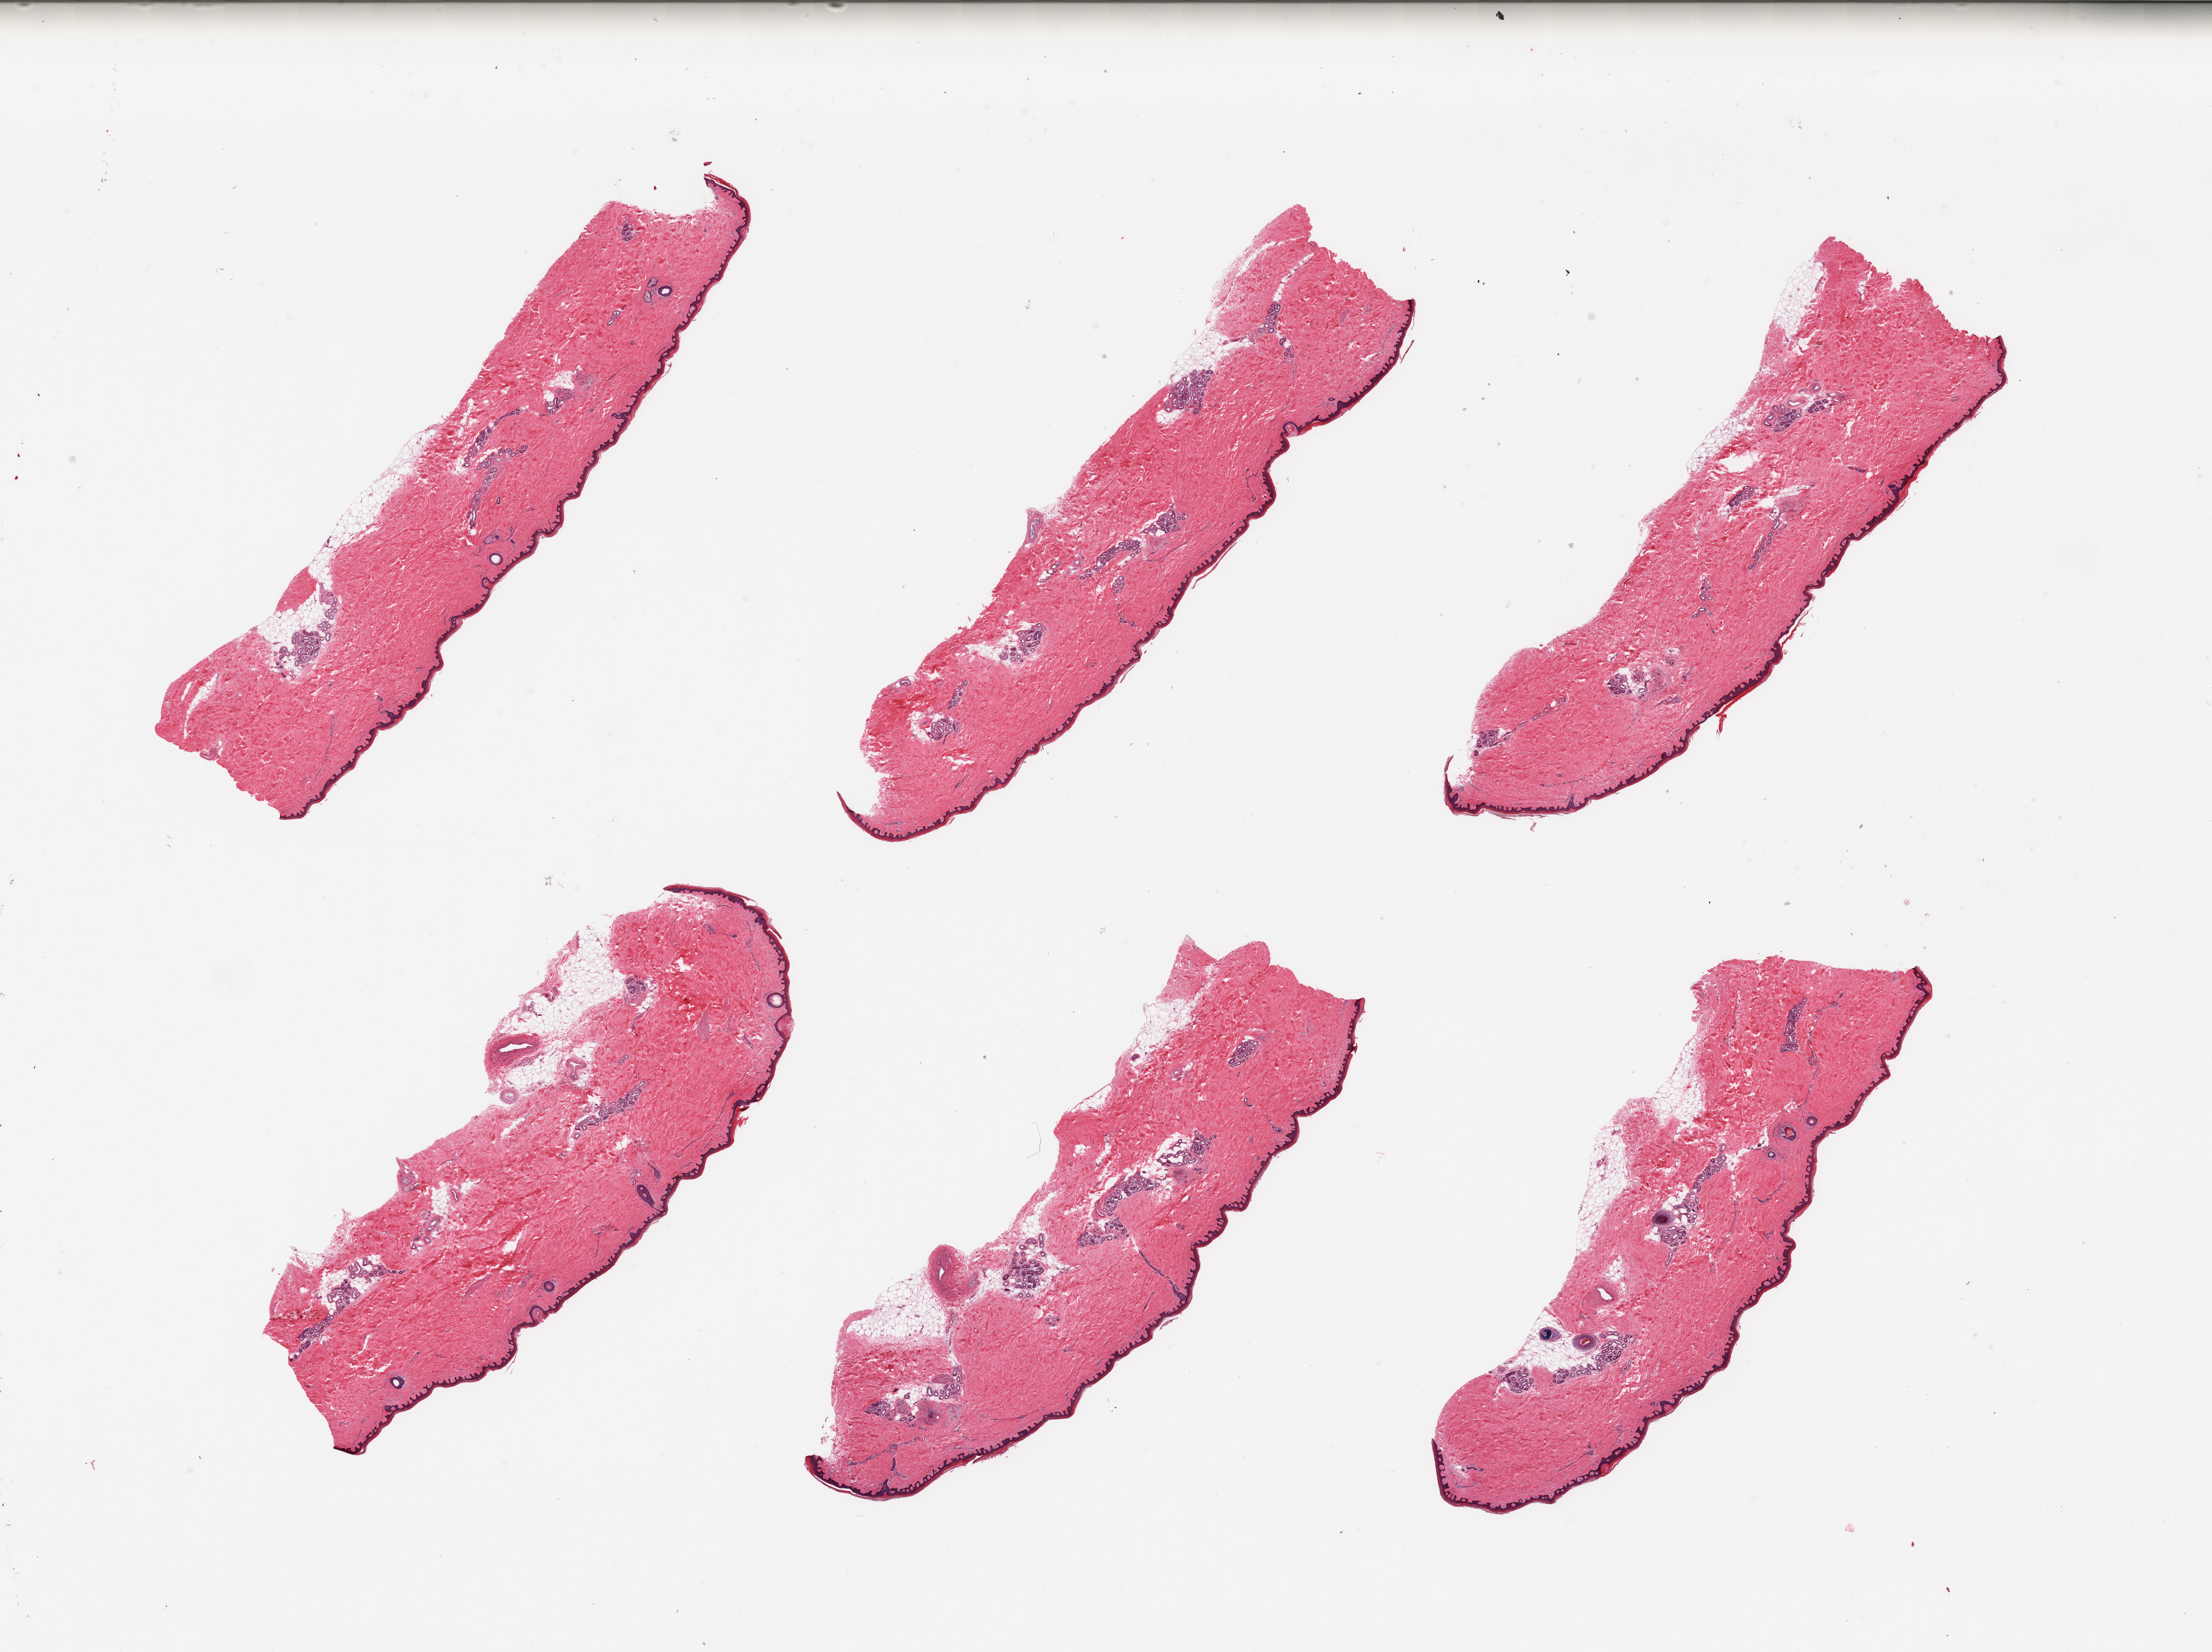
H&E whole-slide image — whole scanned area (about 29.5 x 22.1 mm, slide scanned at 20x) shown as a low-resolution overview; PAXgene-fixed, paraffin-embedded tissue; target tissue: skin of lower leg; tissue donor sample. Donor: male.
• reviewer comment on this tissue sample: 6 pieces, trace adherent fat. Squamous epithelium up to ~30 microns